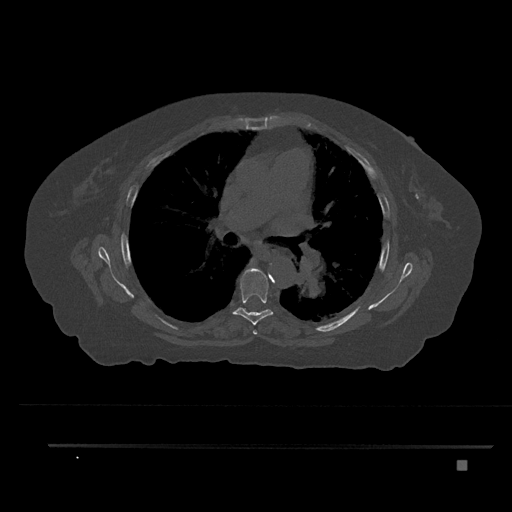
CT including the spine, one axial slice; slice 529 of 797 in the series (ordered by position); reconstruction kernel Br40s/3; bone window (W 1800 / L 400 HU); 0.5 mm slice thickness; 512 × 512 image matrix, field of view 437 × 437 mm. Patient: female, 76 years. From the clinical record (not read from this slice): primary cancer: lung; vertebrae with lytic lesions (as recorded): T11, L3.
Outlined on this slice (semi-automatic segmentation, software-assisted and operator-edited):
- T5 vertebra: box from (x=249, y=268) to (x=257, y=335) px
- T6 vertebra: (x=233, y=267)–(x=274, y=325)